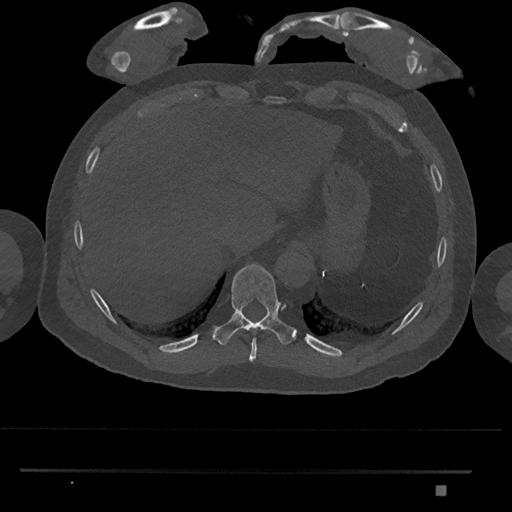
CT including the spine, one axial slice; position 1009 of 1134 along the scan axis; reconstruction kernel Br40s/3; 120 kVp; bone window (W 1800 / L 400 HU); 0.5 mm slice thickness; 512 × 512 image matrix, field of view 429 × 429 mm. Patient: male, 65 years. Case-level facts recorded for this patient, not image findings: primary cancer: prostate.
Annotated regions visible in this slice (semi-automatically segmented with operator editing):
- T10 vertebra: bounding box [x1, y1, x2, y2] px = [212, 264, 296, 345]
- T9 vertebra: [249, 338, 257, 362]